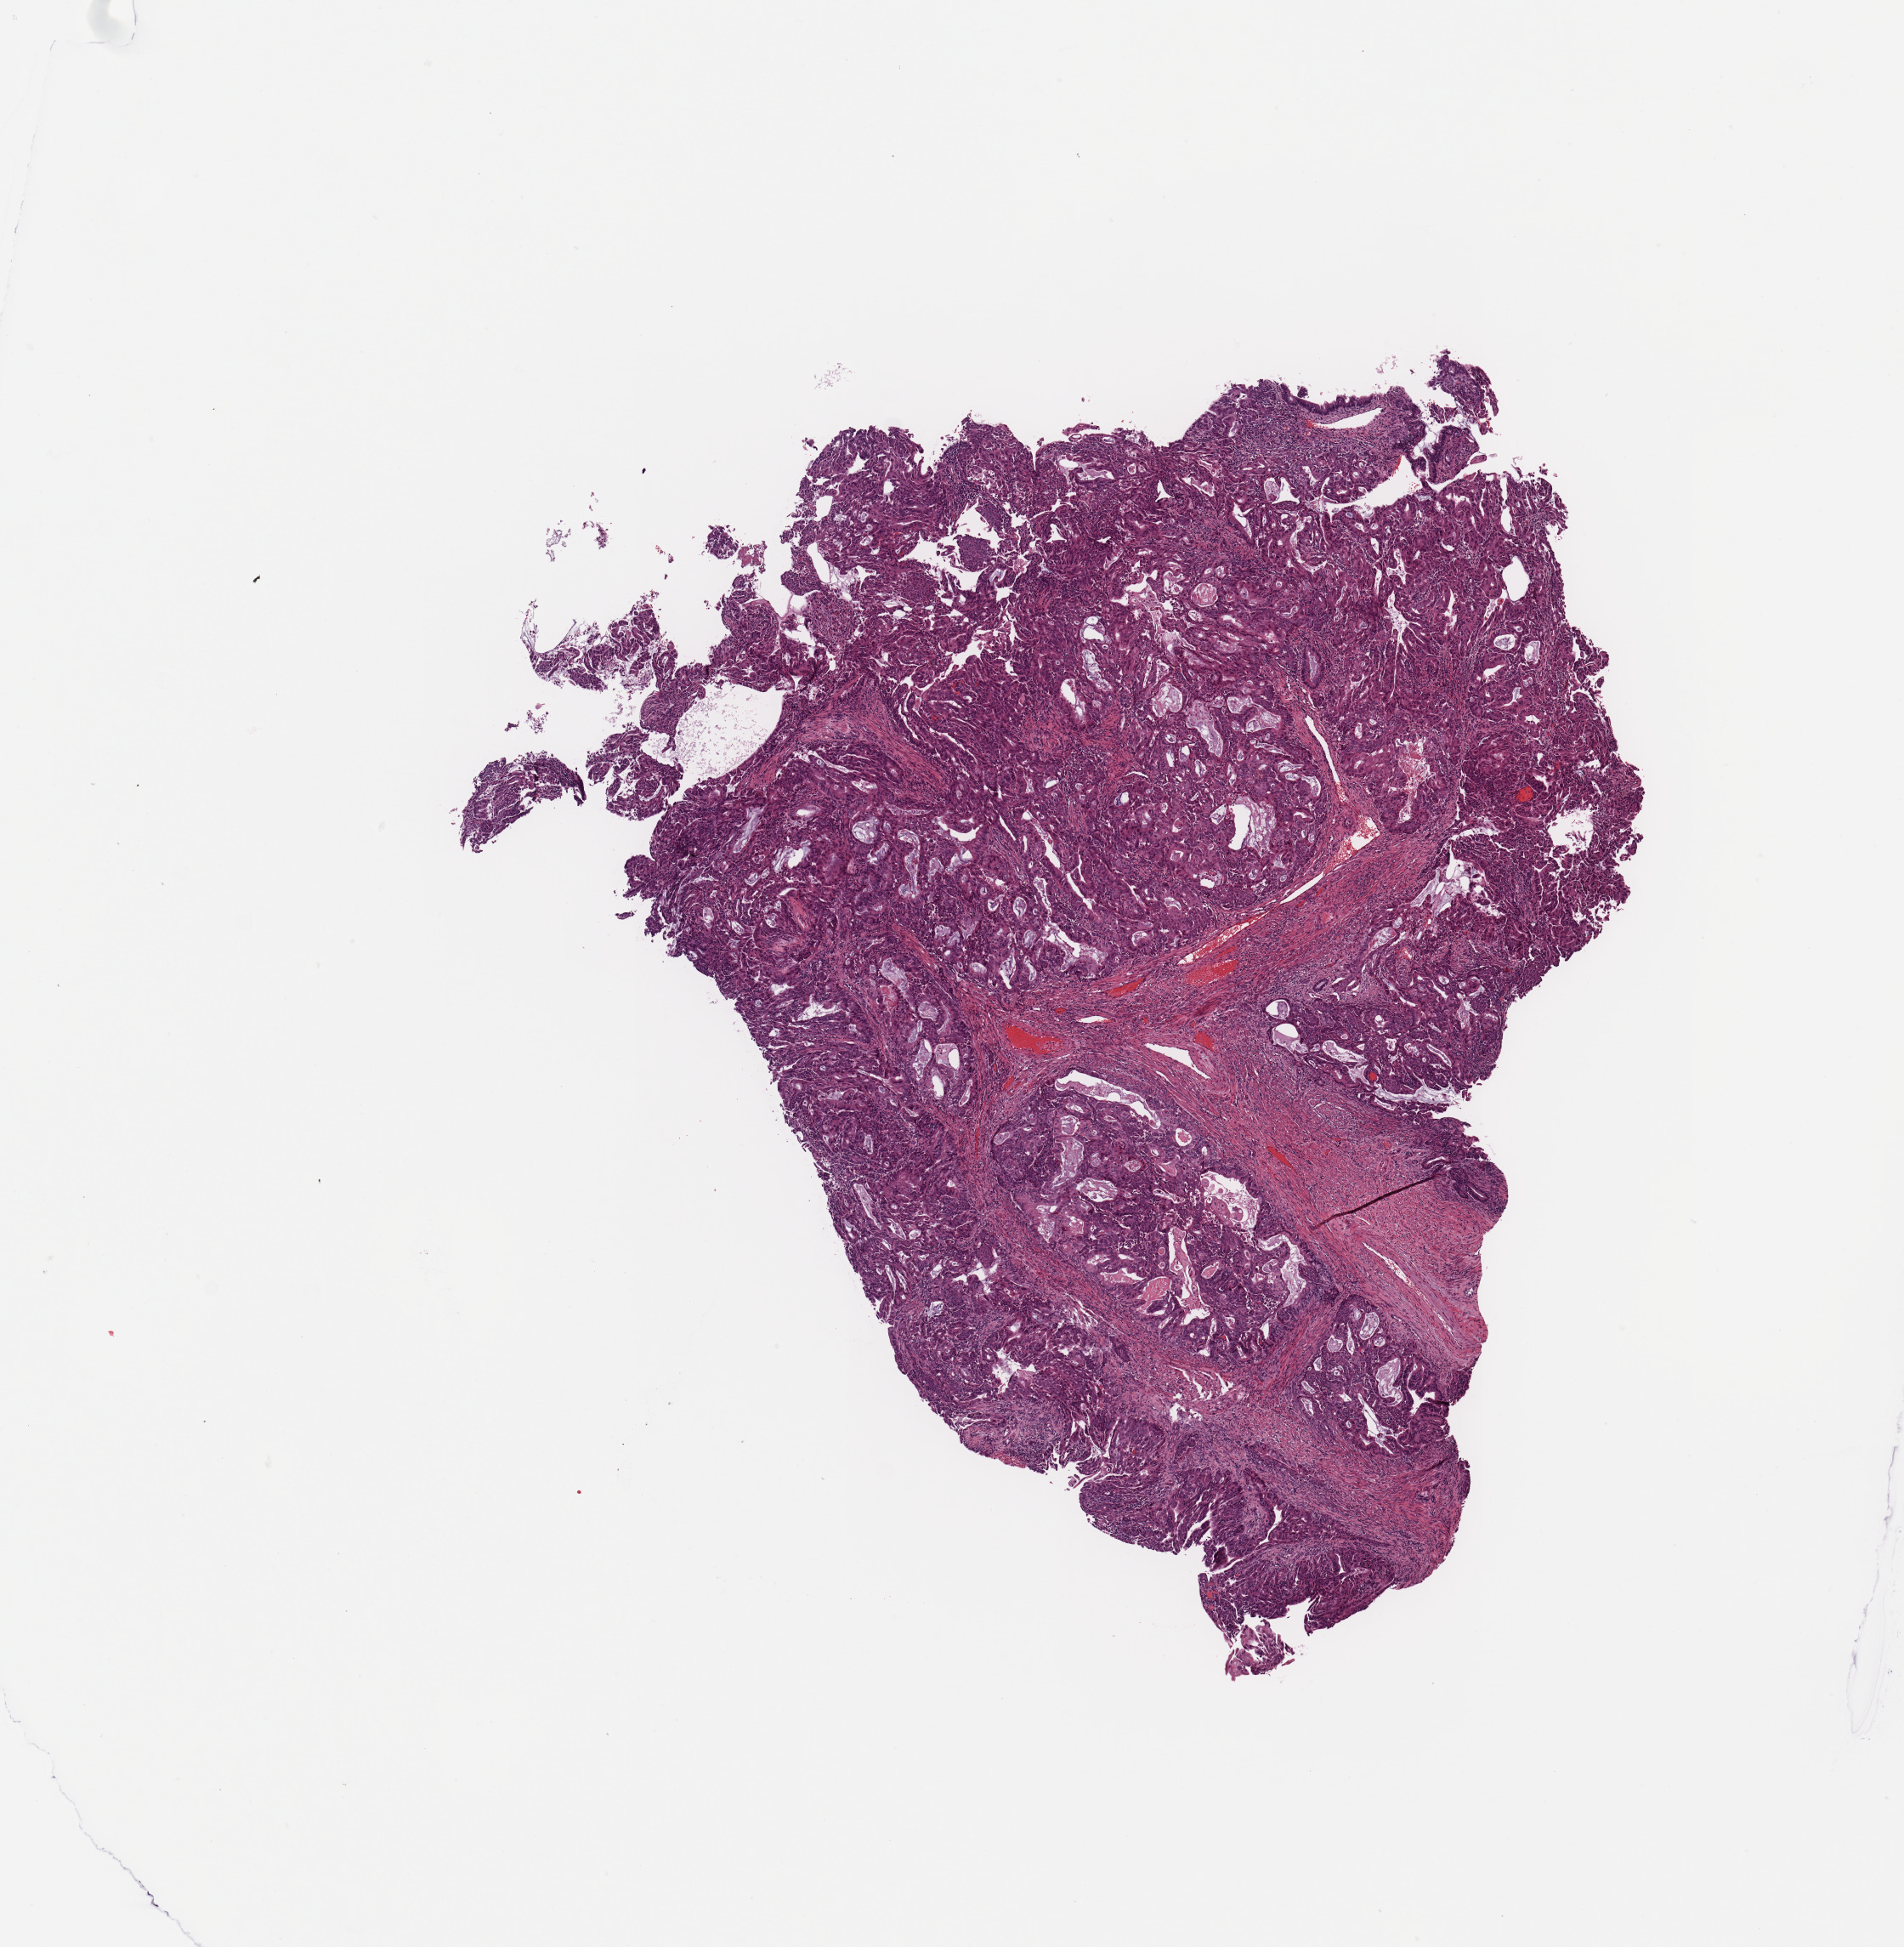
Whole-slide histology image, Hematoxylin and eosin (H&E) stained — whole scanned area (about 8.9 x 9.1 mm) shown as a low-resolution overview; tumour tissue sample, uterus. 54-year-old female patient. Histologic grade: G2 (moderately differentiated).
• diagnosis: Endometrioid adenocarcinoma, NOS
• AJCC pathologic stage: IIIB